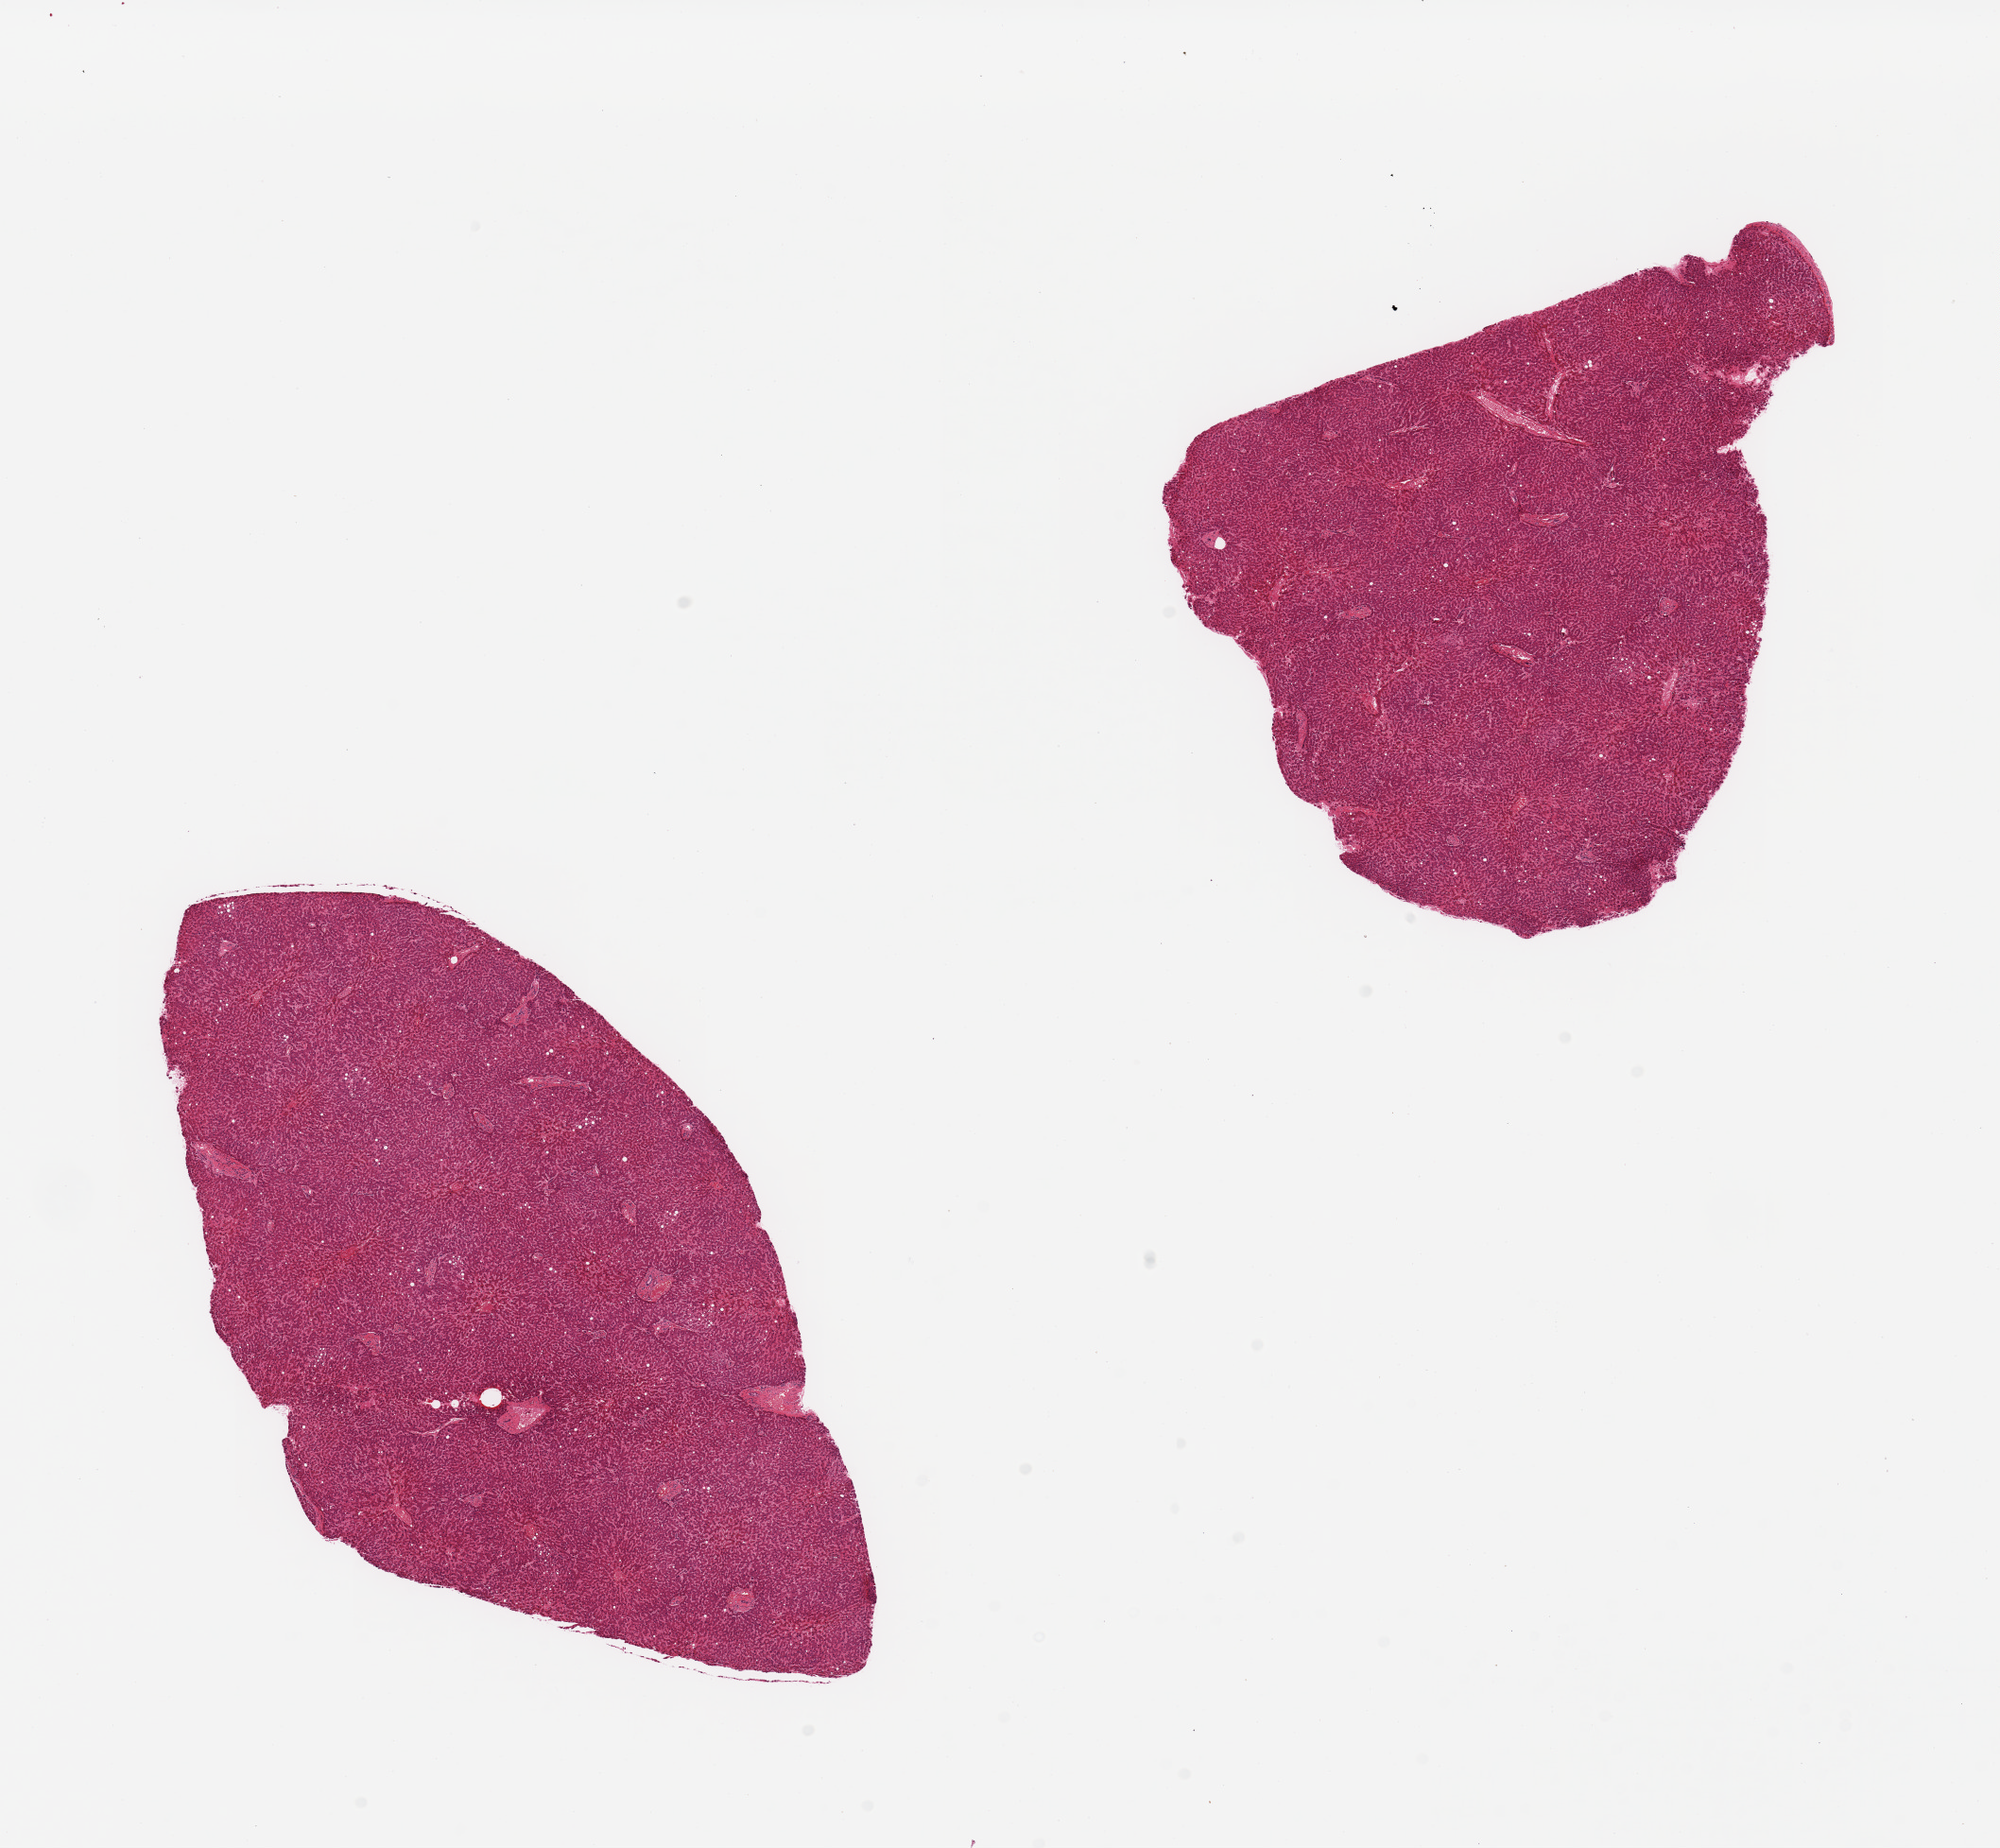
H&E whole-slide image, brightfield — low-resolution overview of the scanned area, about 16.7 x 15.5 mm. PAXgene-fixed, paraffin-embedded tissue. Target tissue: liver. Donor tissue sample. Donor sex: male.
- review note (as recorded): 2 pieces; <2% macrovesicular fat; no fibrosis or inflammation